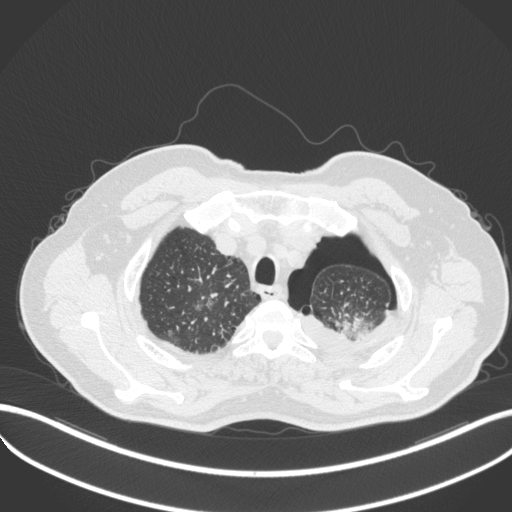
Chest CT, one axial slice. Slice 426 of 466 in the series (ordered by position). Lung window (W 1500 / L -600 HU). 1 mm slice thickness. 512 × 512 image matrix, field of view 400 × 400 mm. Male patient, age 76 years. Case-level facts recorded for this patient, not image findings: clinical TNM (as recorded): T3 N0 M1b.
Structures marked on this image (rectangle marked by the reading radiologist):
- lung tumour (recorded histology: adenocarcinoma): box from (x=331, y=310) to (x=373, y=343) px